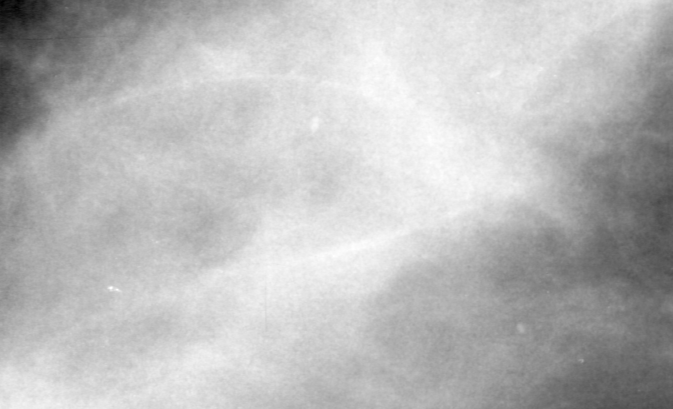
Crop from a digitized film mammogram around one marked abnormality, left breast, CC view.
Marked abnormality: calcifications, morphology pleomorphic, distribution segmental; BI-RADS assessment category 4; subtlety rating 2 on a 1 (subtle) to 5 (obvious) scale; pathology result (as recorded, not read from the image): benign.